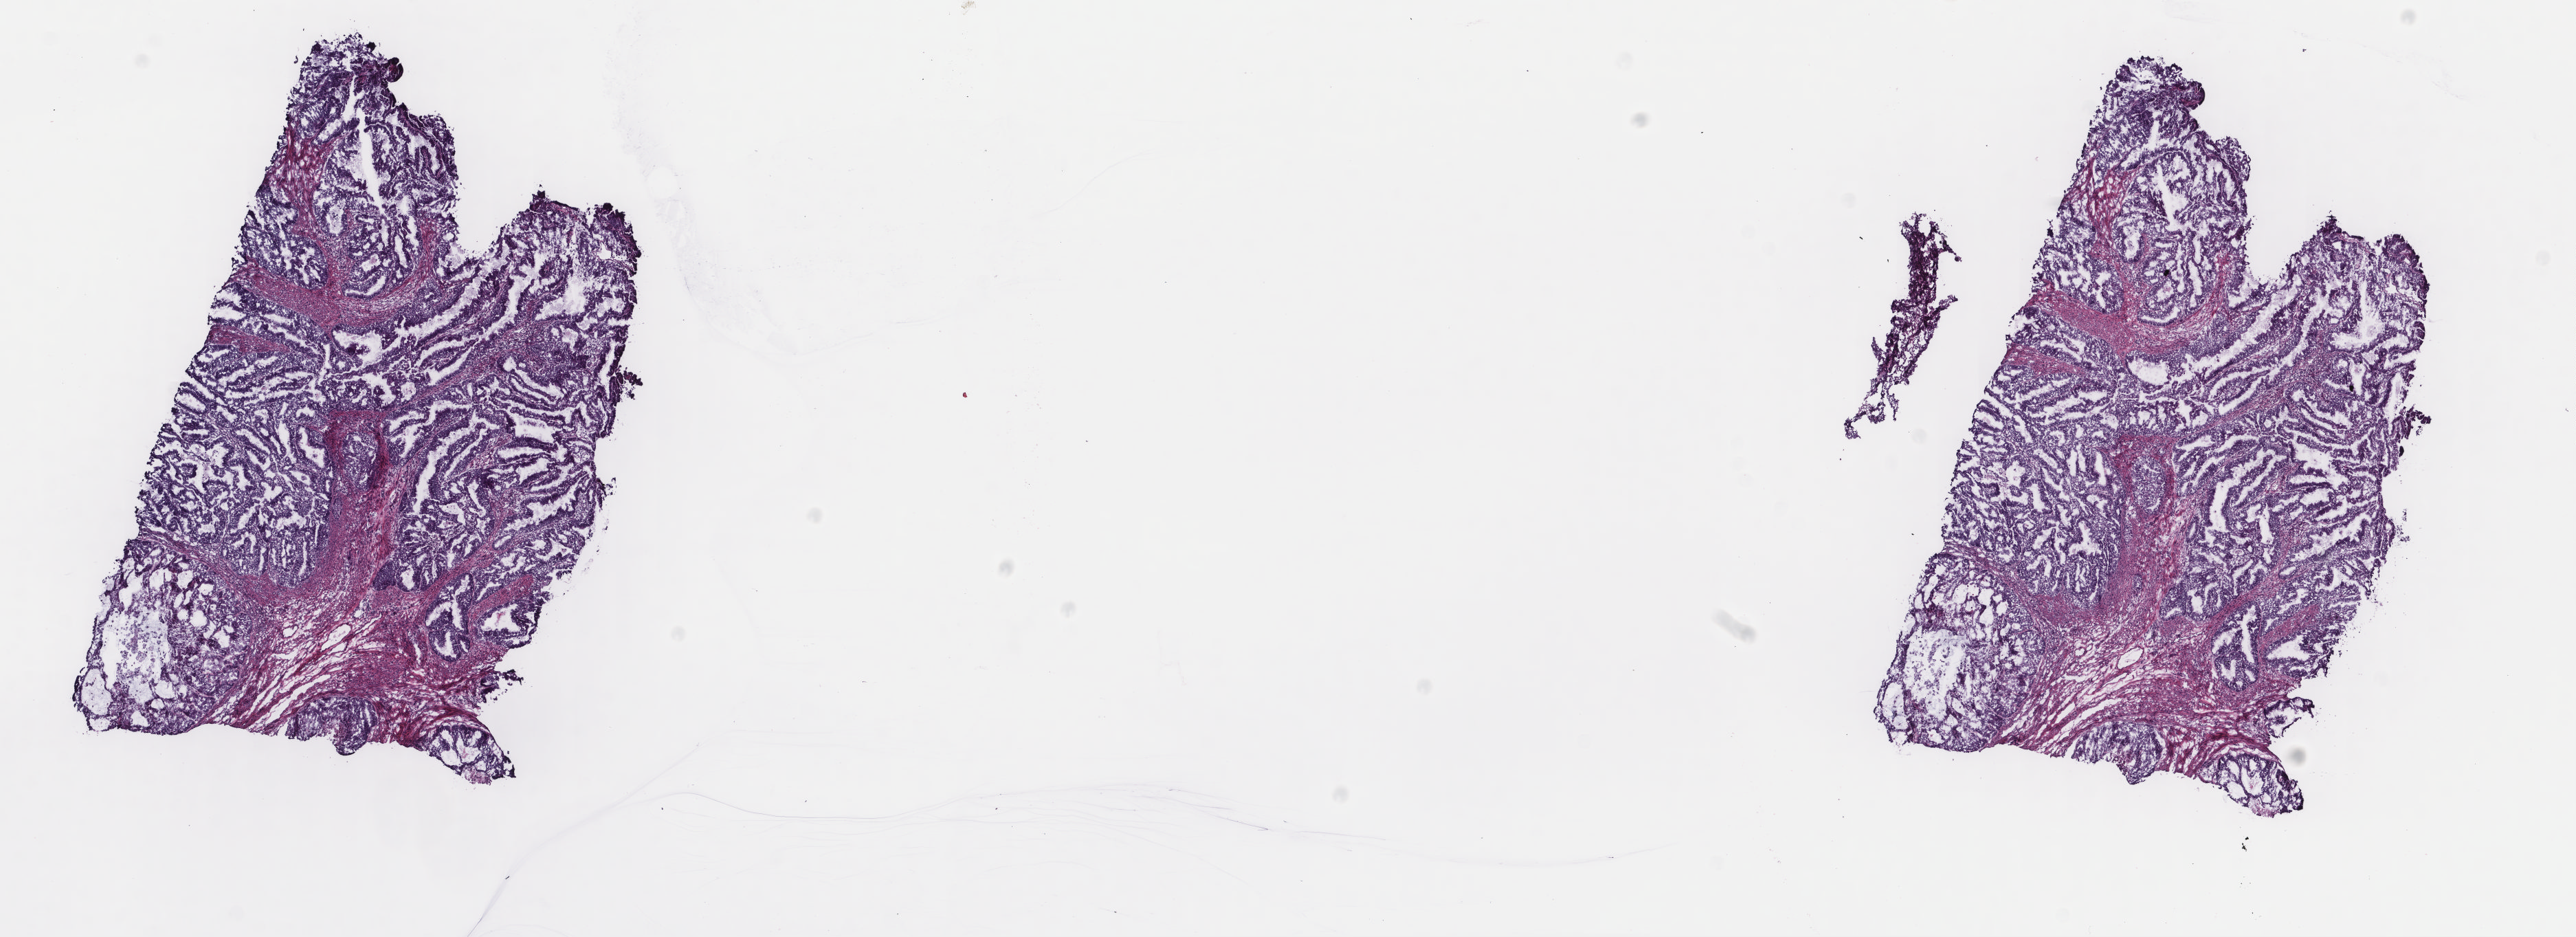
Whole-slide histology image, H&E, low-resolution overview of the scanned area, about 14.9 x 5.4 mm (slide scanned at 40x), frozen section from the top of the tissue portion, primary tumour sample from the uterus. Patient: female, age at initial diagnosis 69 years. Histologic grade: G1 (well differentiated). Composition of this section per pathologist review: tumour cells 75%, tumour nuclei 70%, normal cells 25%, stromal cells 0%, necrosis 0%. Inflammatory infiltration, as recorded: lymphocyte infiltration 0%, monocyte infiltration 0%, neutrophil infiltration 0%.
Lymph nodes positive (case pathology): 0 of 16 examined. FIGO stage: IB. Pathologic diagnosis: Endometrioid adenocarcinoma, NOS.